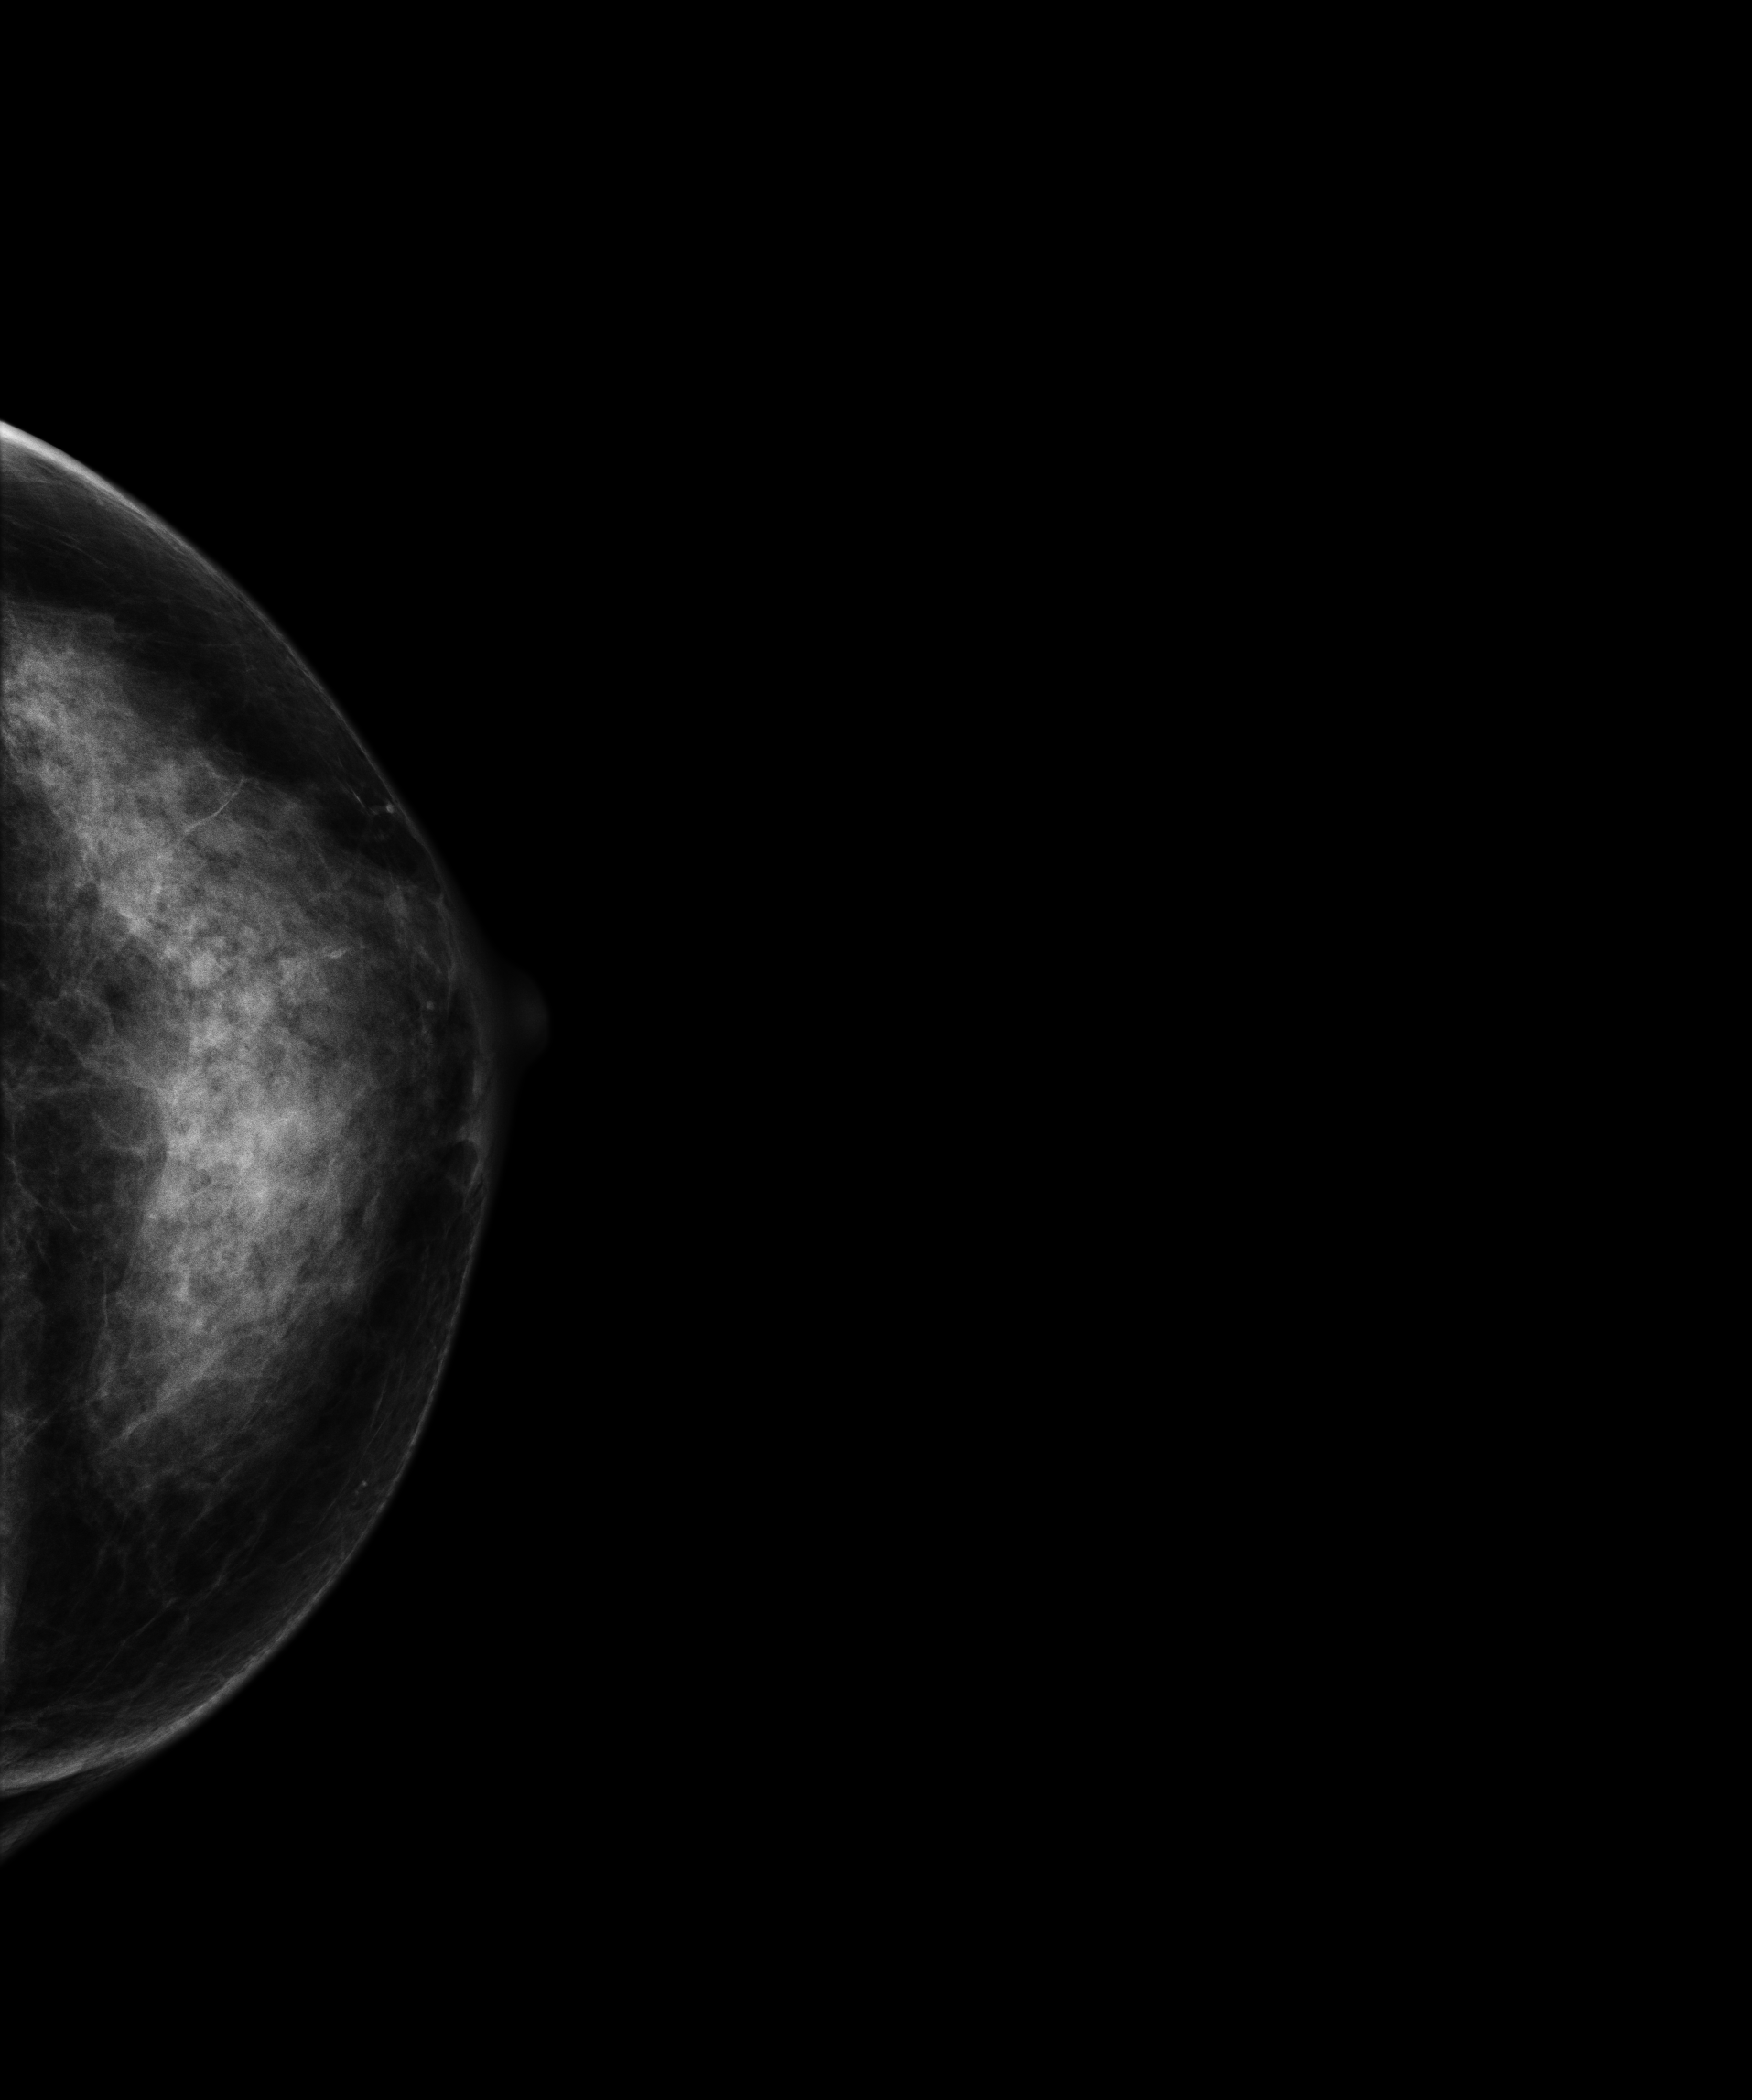
Screening examination; compressed breast thickness 48 mm. Patient aged 55 years (female).
Image type: full-field digital mammogram. Breast: left. Projection: craniocaudal (CC) view.